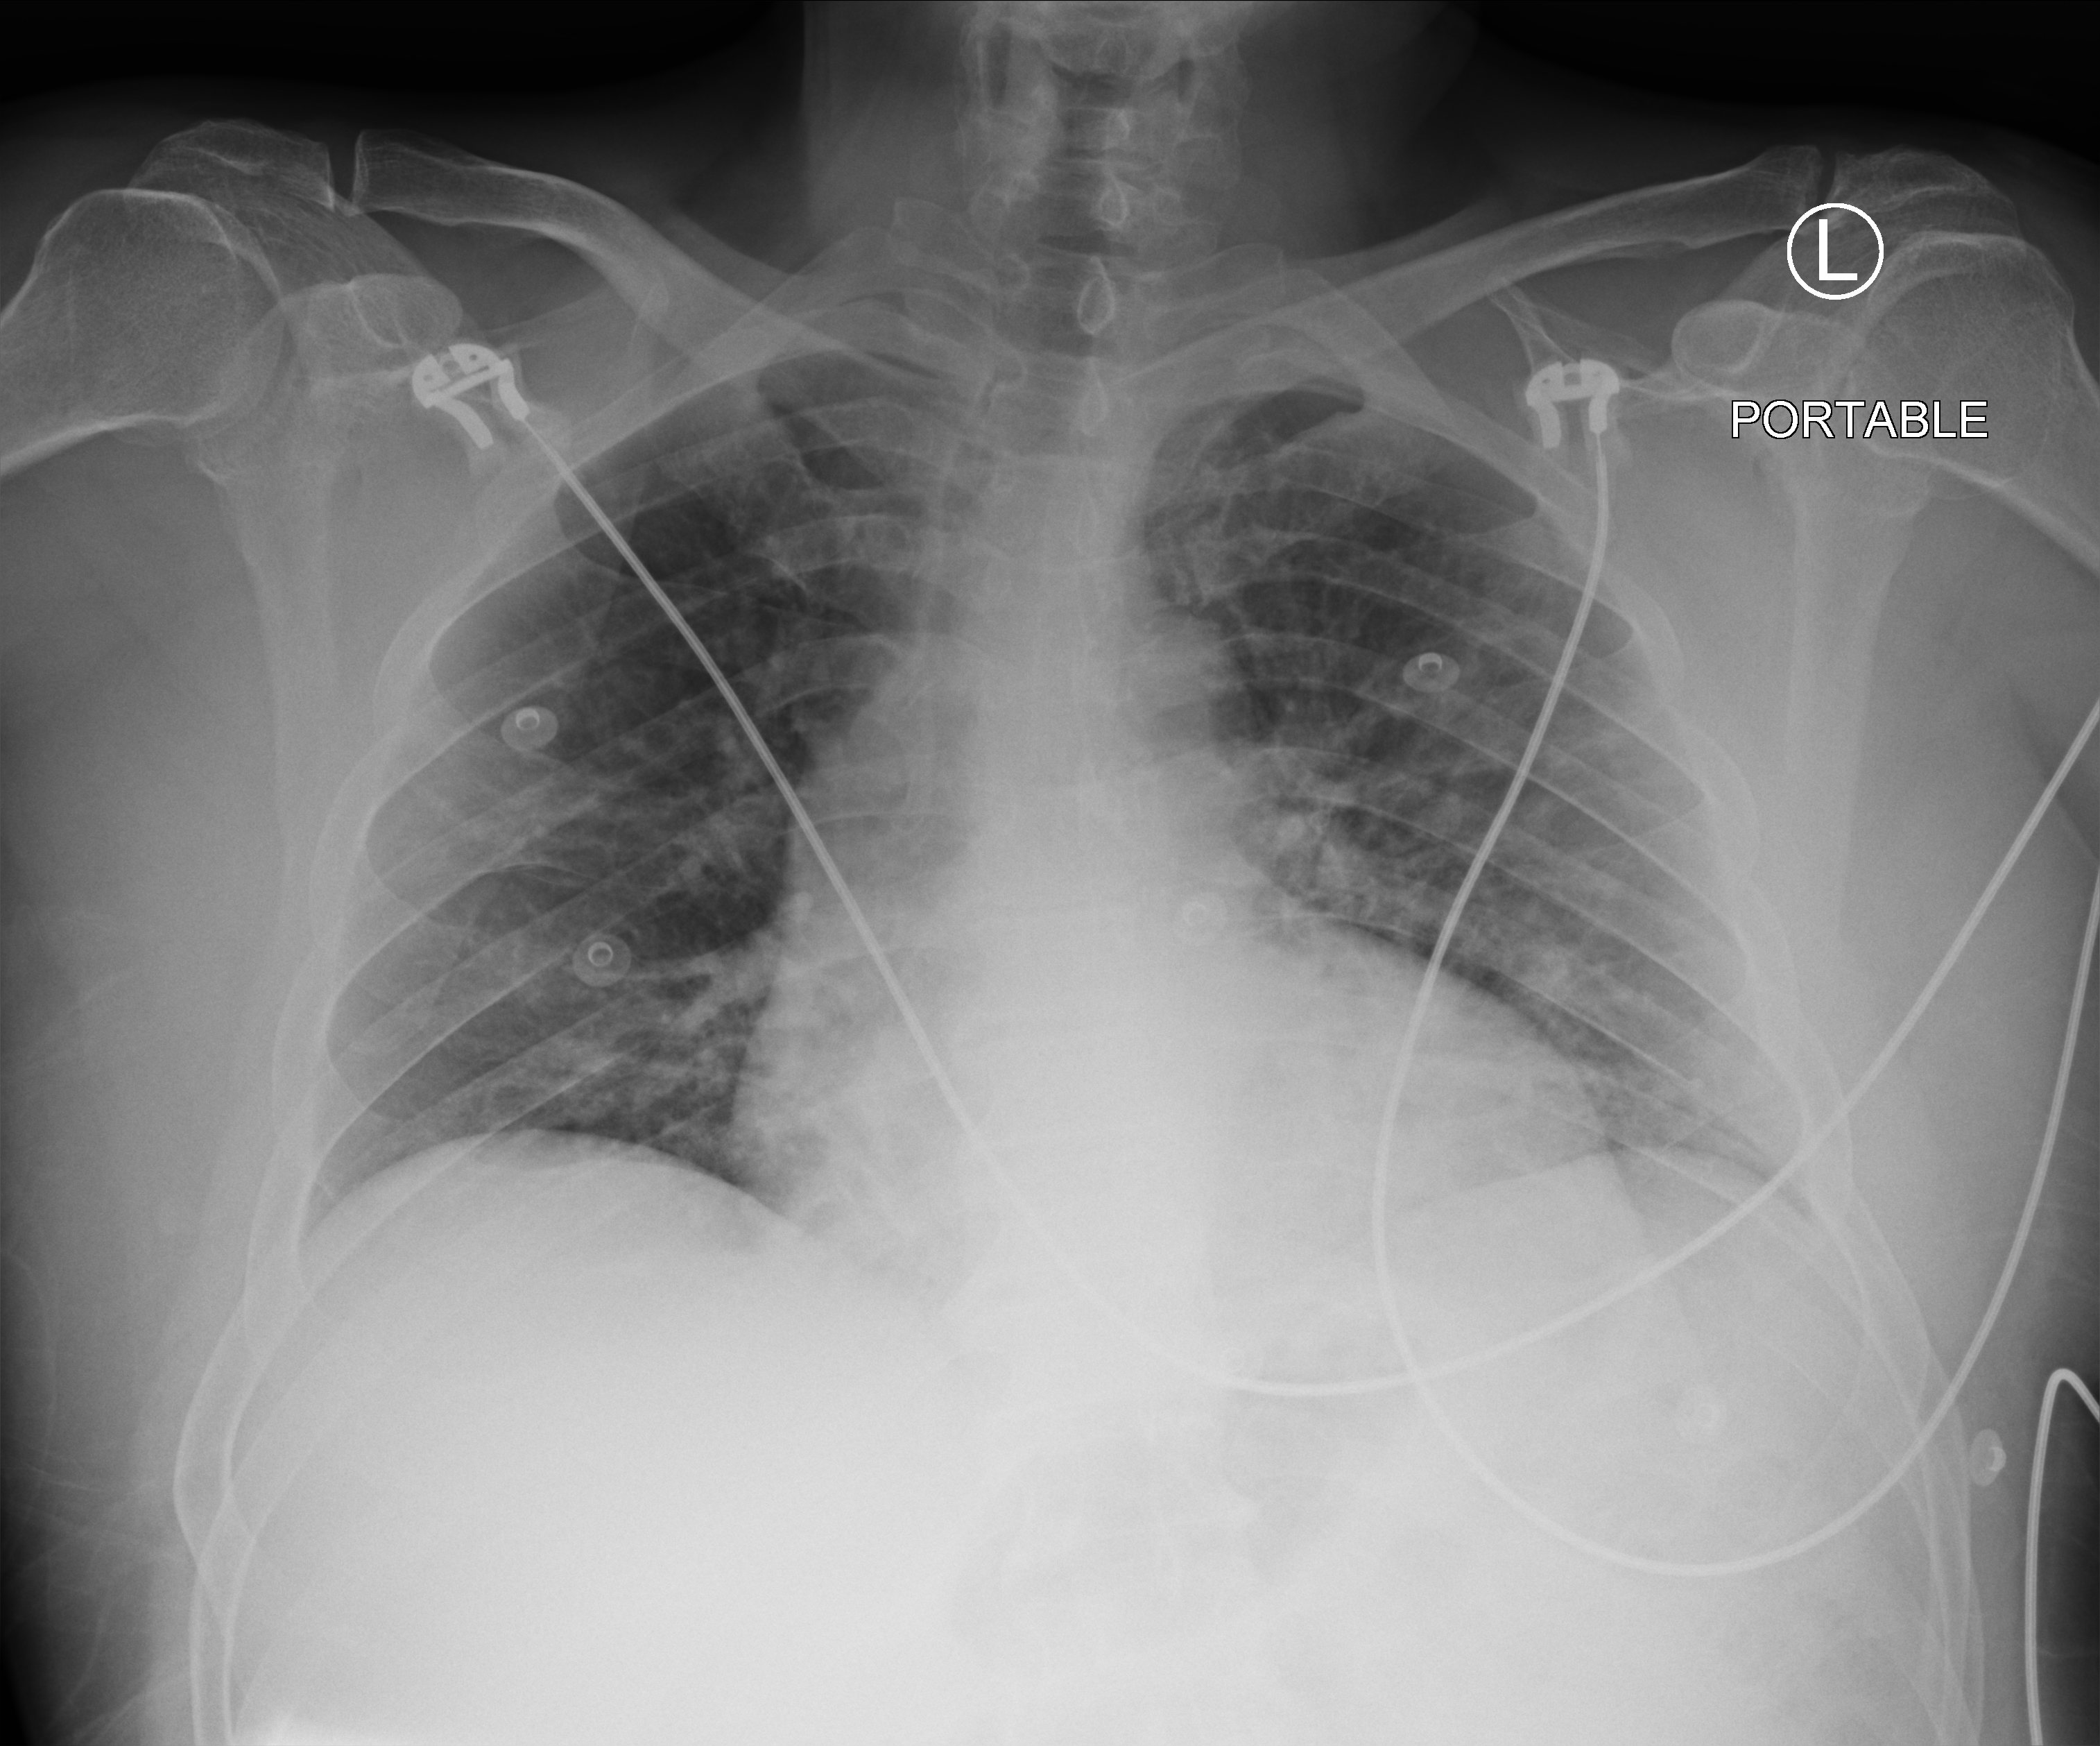
Portable chest radiograph, anteroposterior (AP) projection. Patient hospitalised with COVID-19; male, aged 18–59 years.
From the hospital-stay record, not from the radiograph (when in the stay this image was taken is not recorded): chronic kidney disease (admission record): no.